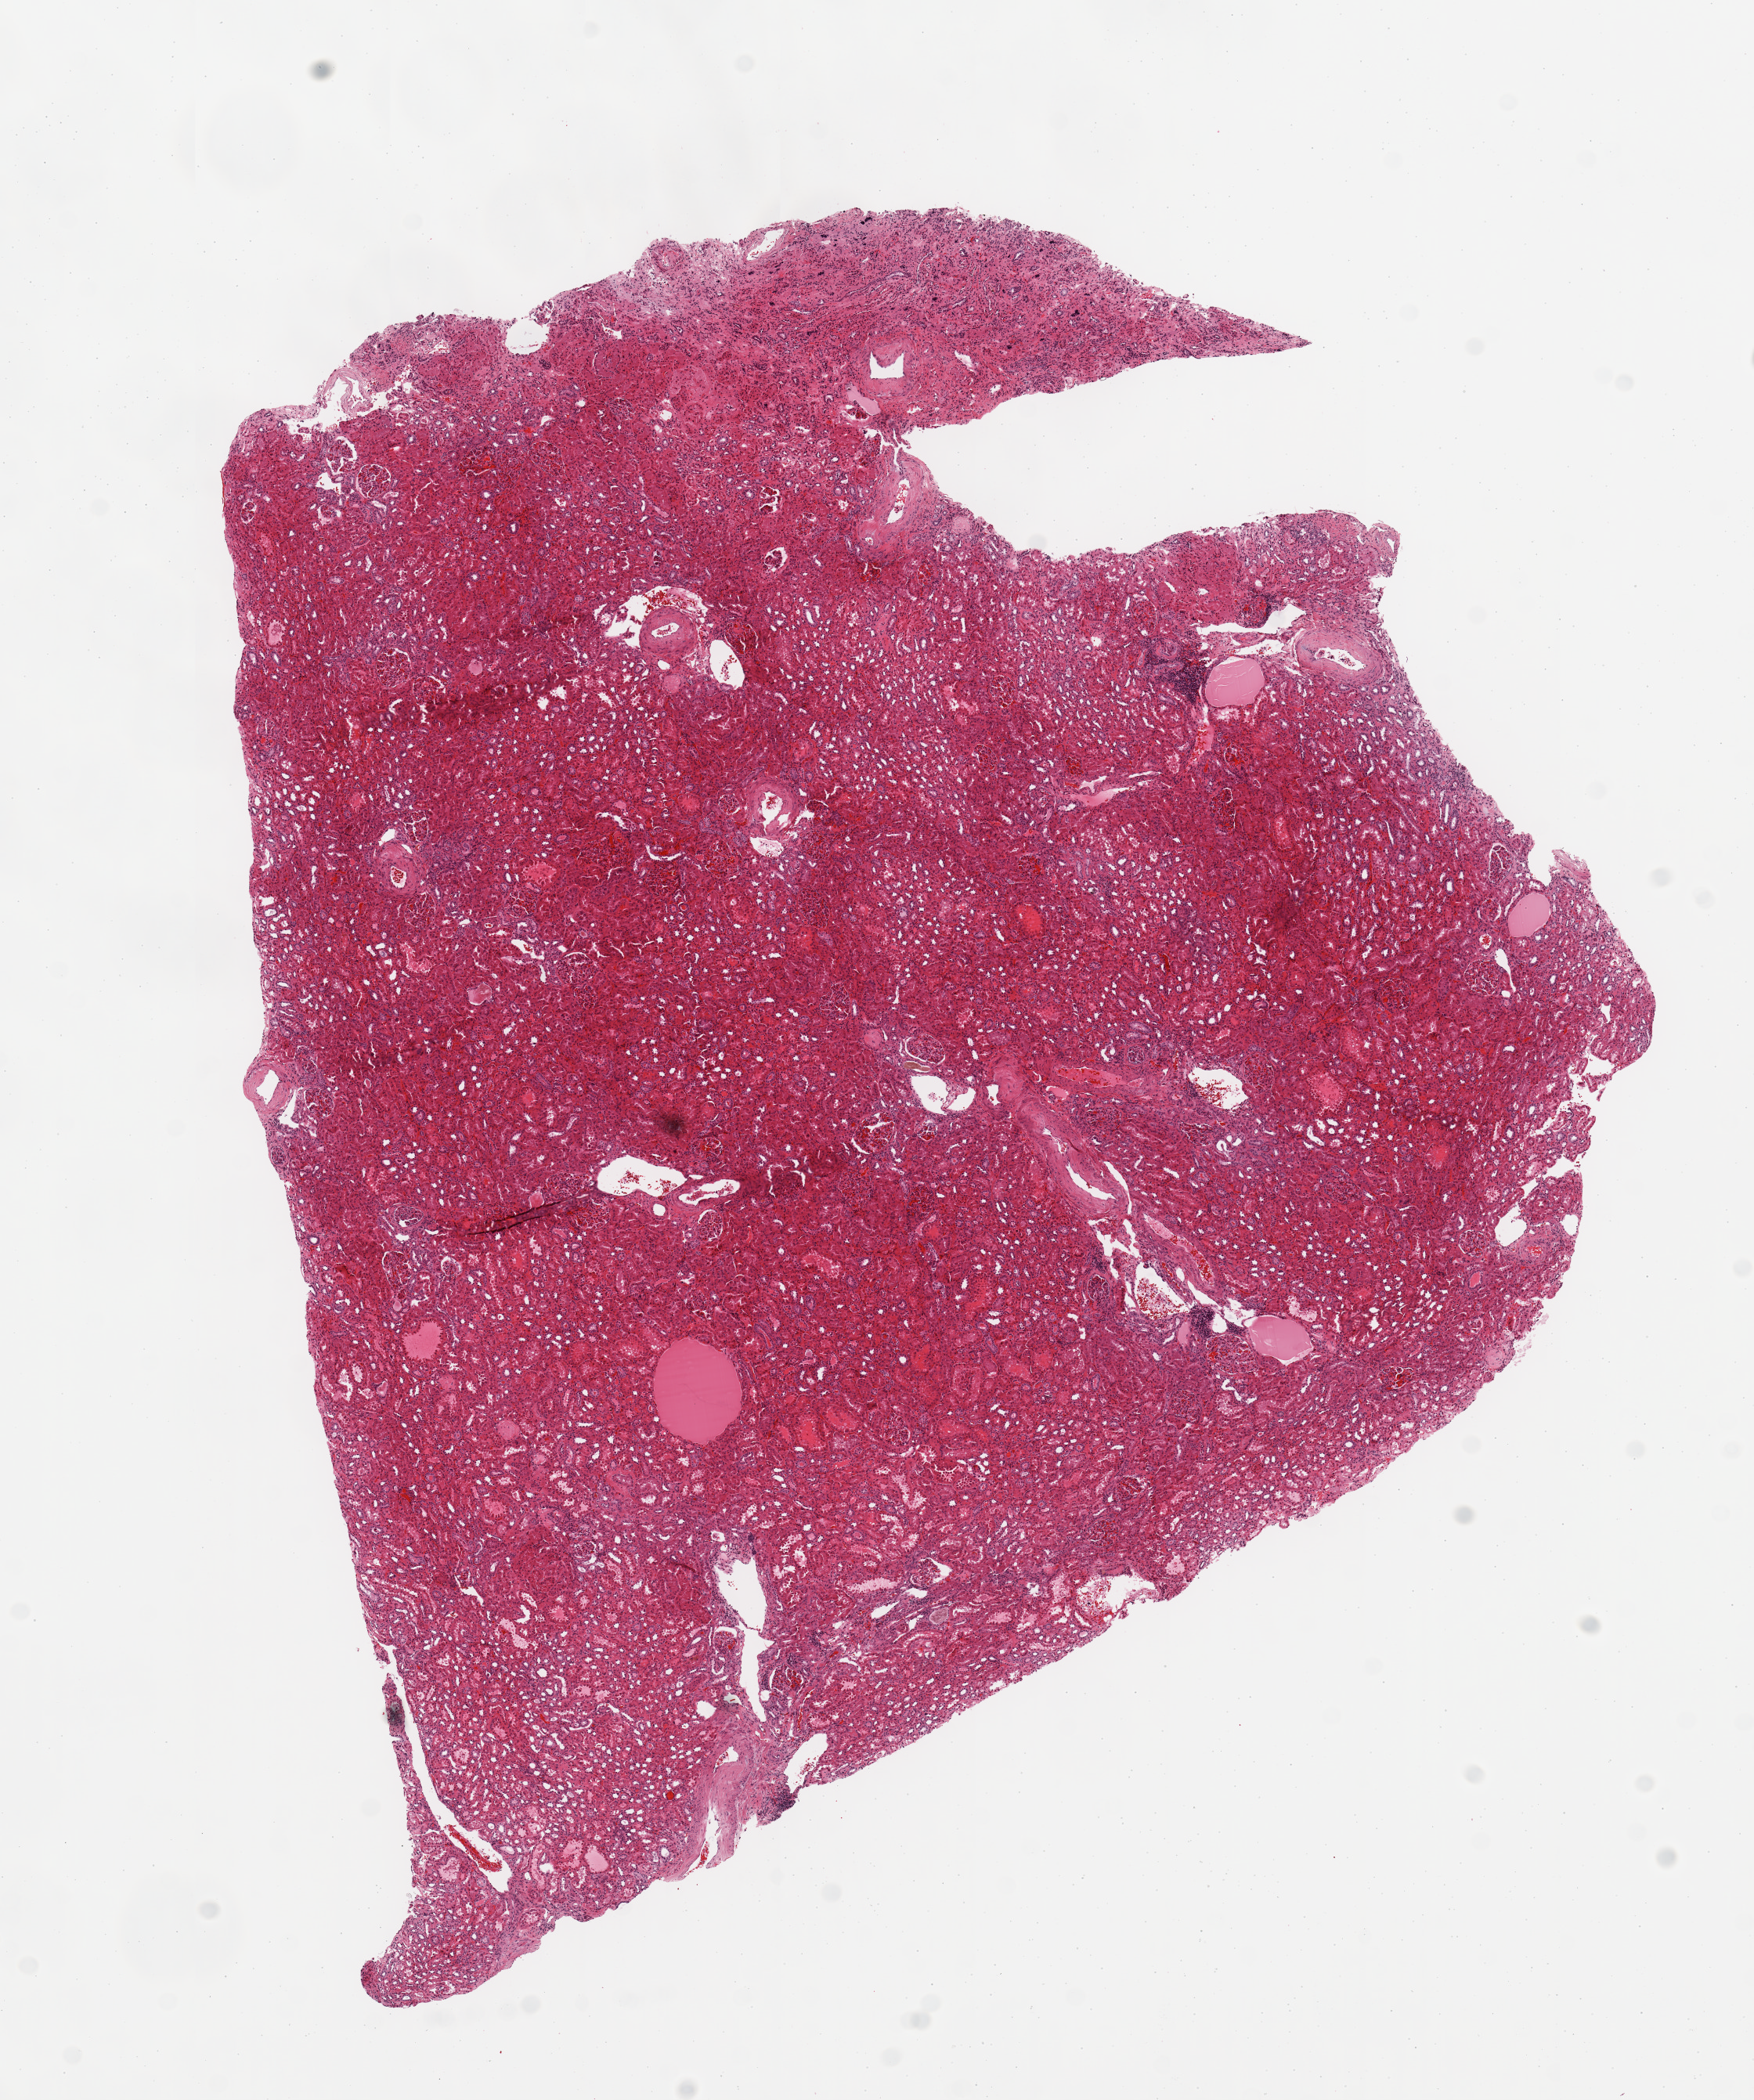
Hematoxylin and eosin (H&E) stained whole-slide image — shown as a low-resolution overview of the whole scanned area (about 8.9 x 10.6 mm). Normal (non-tumour) tissue sample, sampled site: kidney. 75-year-old female patient.
This section: normal (non-tumour) tissue from the same patient. Patient diagnosis: Renal cell carcinoma, NOS.